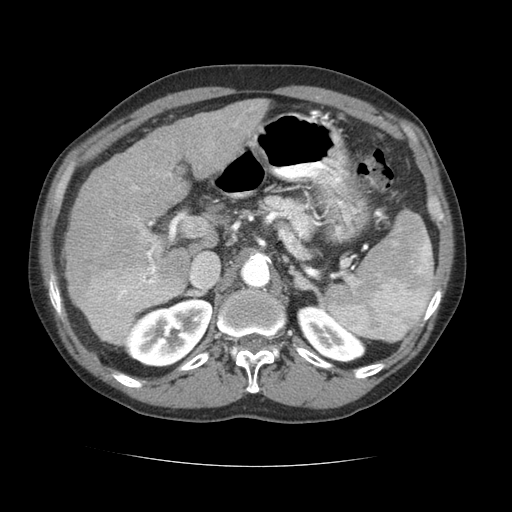
Contrast-enhanced abdominal CT (liver protocol), one axial slice. Slice 43 of 69 in the series (ordered by position). Reconstruction kernel STANDARD. 120 kVp. Soft-tissue window (W 400 / L 40 HU). 2.5 mm slice thickness. 512 × 512 image matrix, field of view 360 × 360 mm. Case-level facts recorded for this patient, not image findings: diagnosis: hepatocellular carcinoma (patient treated with transarterial chemoembolisation; whether this scan precedes or follows treatment is not stated here); TNM stage (as recorded): Stage-II; Child-Pugh class: B; tumour differentiation: poorly differentiated.
Annotated regions visible in this slice (semi-automatic segmentation, software-assisted and operator-edited):
- liver parenchyma outside the tumour (the mass and vessels are separate outlines, so this box may not span the whole liver): box from (x=64, y=98) to (x=268, y=320) px
- mass: (x=77, y=264)–(x=179, y=344)
- liver vessels: (x=133, y=174)–(x=171, y=280)